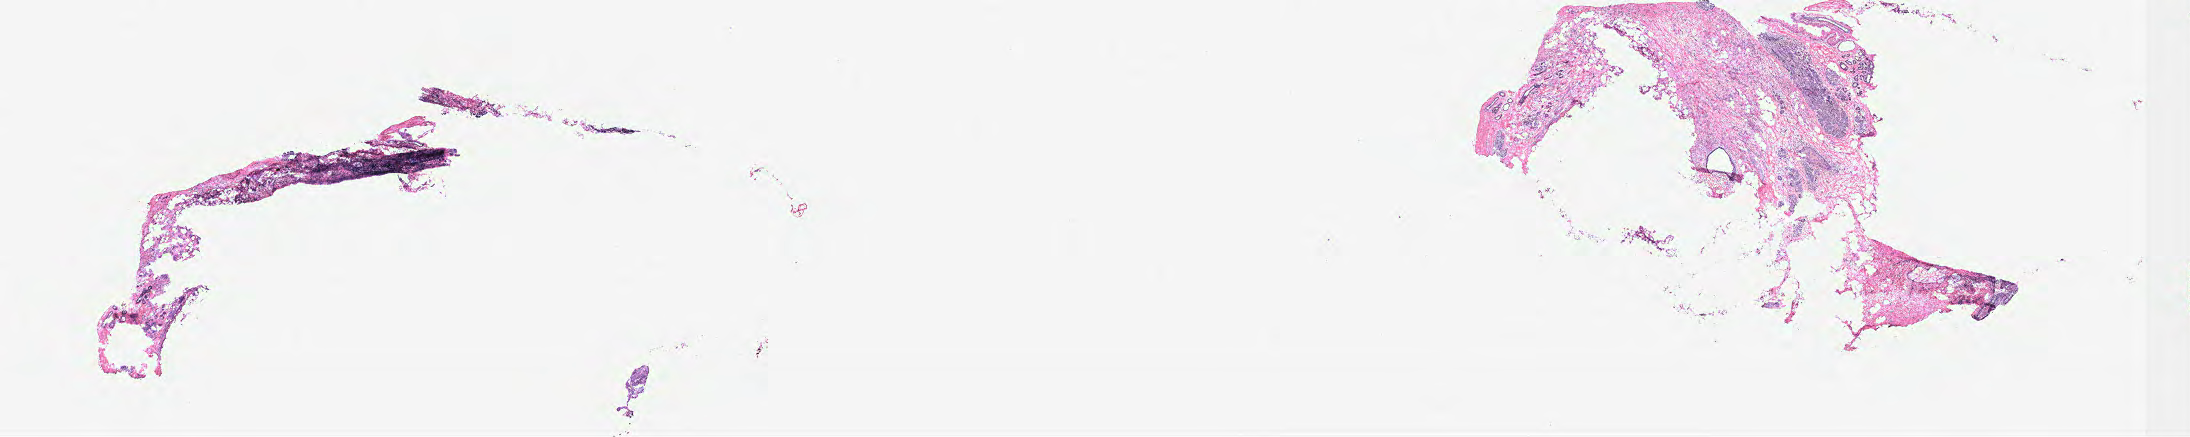
Whole-slide histology image, H&E, a low-resolution overview of the entire scanned area, about 35.1 x 7.0 mm (slide scanned at 40x), breast, tissue type not recorded.
Patient diagnosis (cohort enrolment): breast cancer (breast).